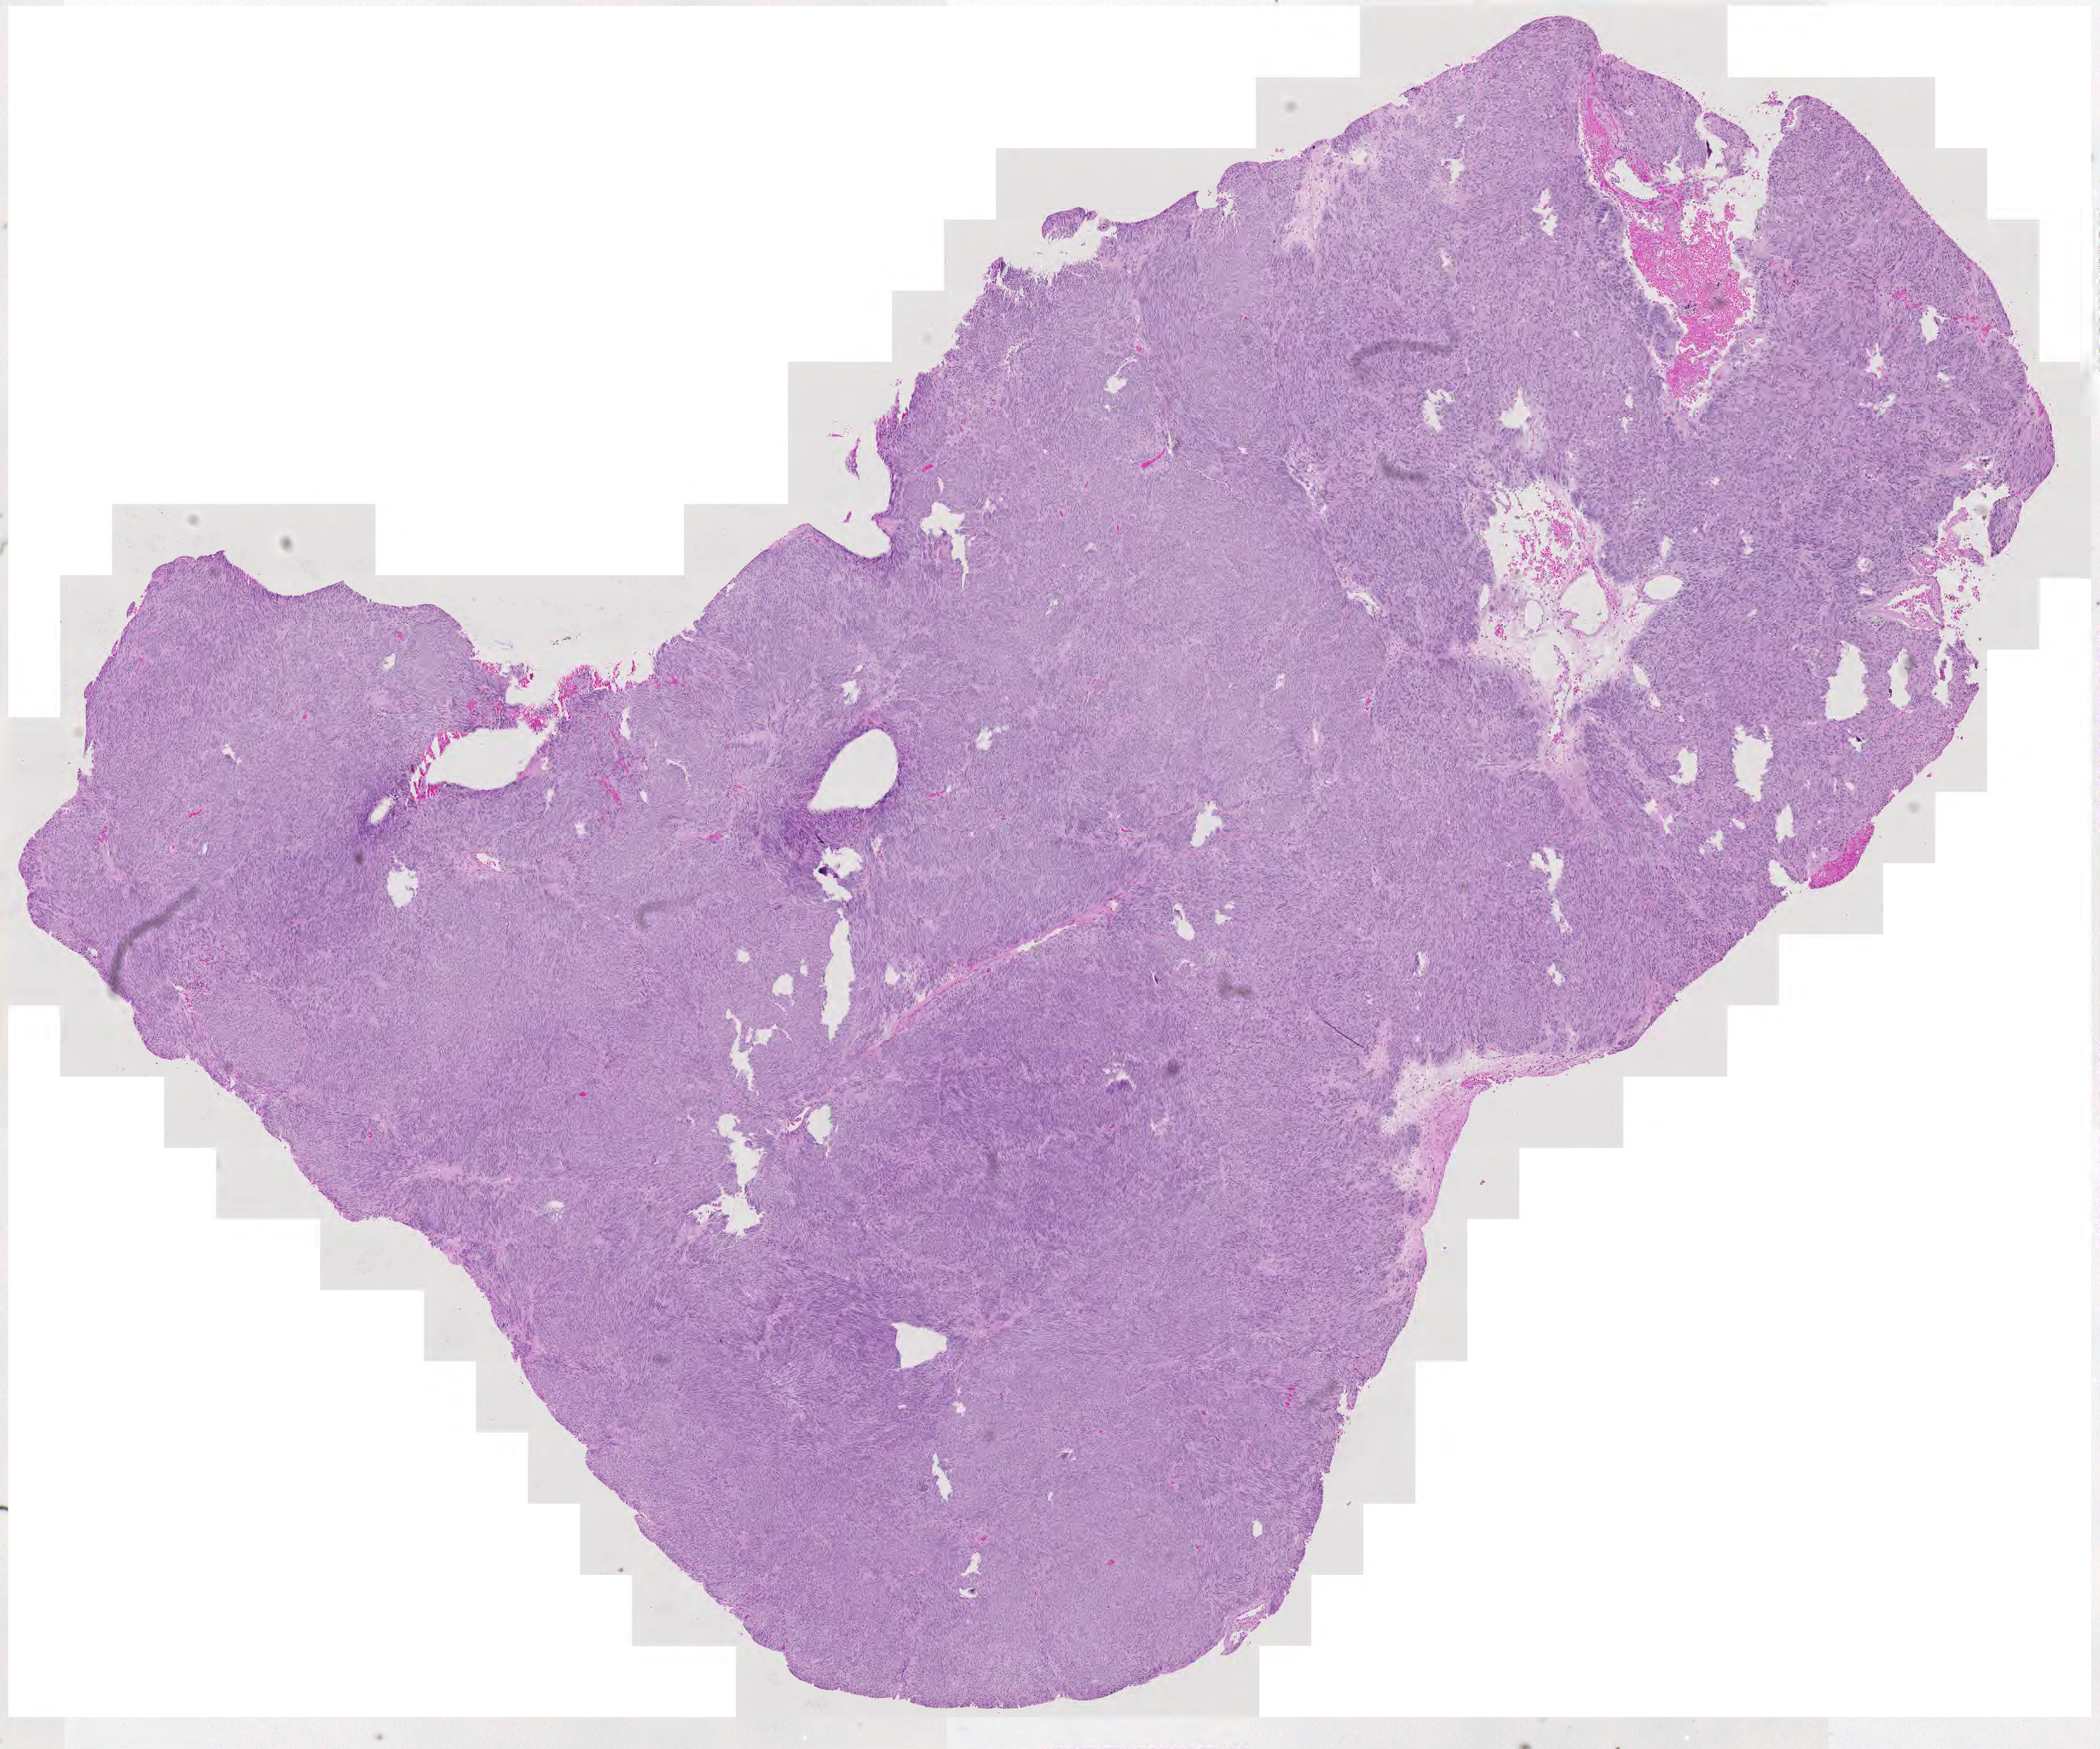
Whole-slide histology image, H&E-stained — a low-resolution overview of the entire scanned area, about 12.5 x 10.4 mm (from a 20x scan). Patient: male, age 87 years.
Patient diagnosis (cohort enrolment): sarcoma (site not recorded at cohort level).